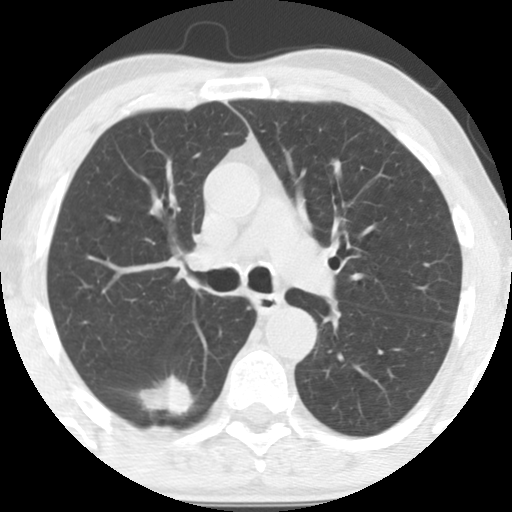
Axial slice from a low-dose chest CT screening exam. First (baseline) screen. Lung window (W 1500 / L -600 HU). Standard (soft-tissue) reconstruction kernel (STANDARD). Slice 46 of 135 in the series. 512 × 512 image matrix. Male, age 64 years at enrolment. Current smoker at enrolment.
• Lesion marked by an expert reader, bounding box (x1, y1, x2, y2) in pixels: (120, 365, 195, 432).
• The exam's reader record, not a measurement of the box and not confirmed to be the same lesion: non-calcified nodule or mass ≥4 mm, right lower lobe, 36 × 26 mm, spiculated (stellate) margins, soft tissue attenuation.
• Lung cancer was diagnosed 20 days after this screen: adenocarcinoma, NOS, right lower lobe, moderately differentiated (G2), stage IA (AJCC 6th edition), 28 mm at pathology.